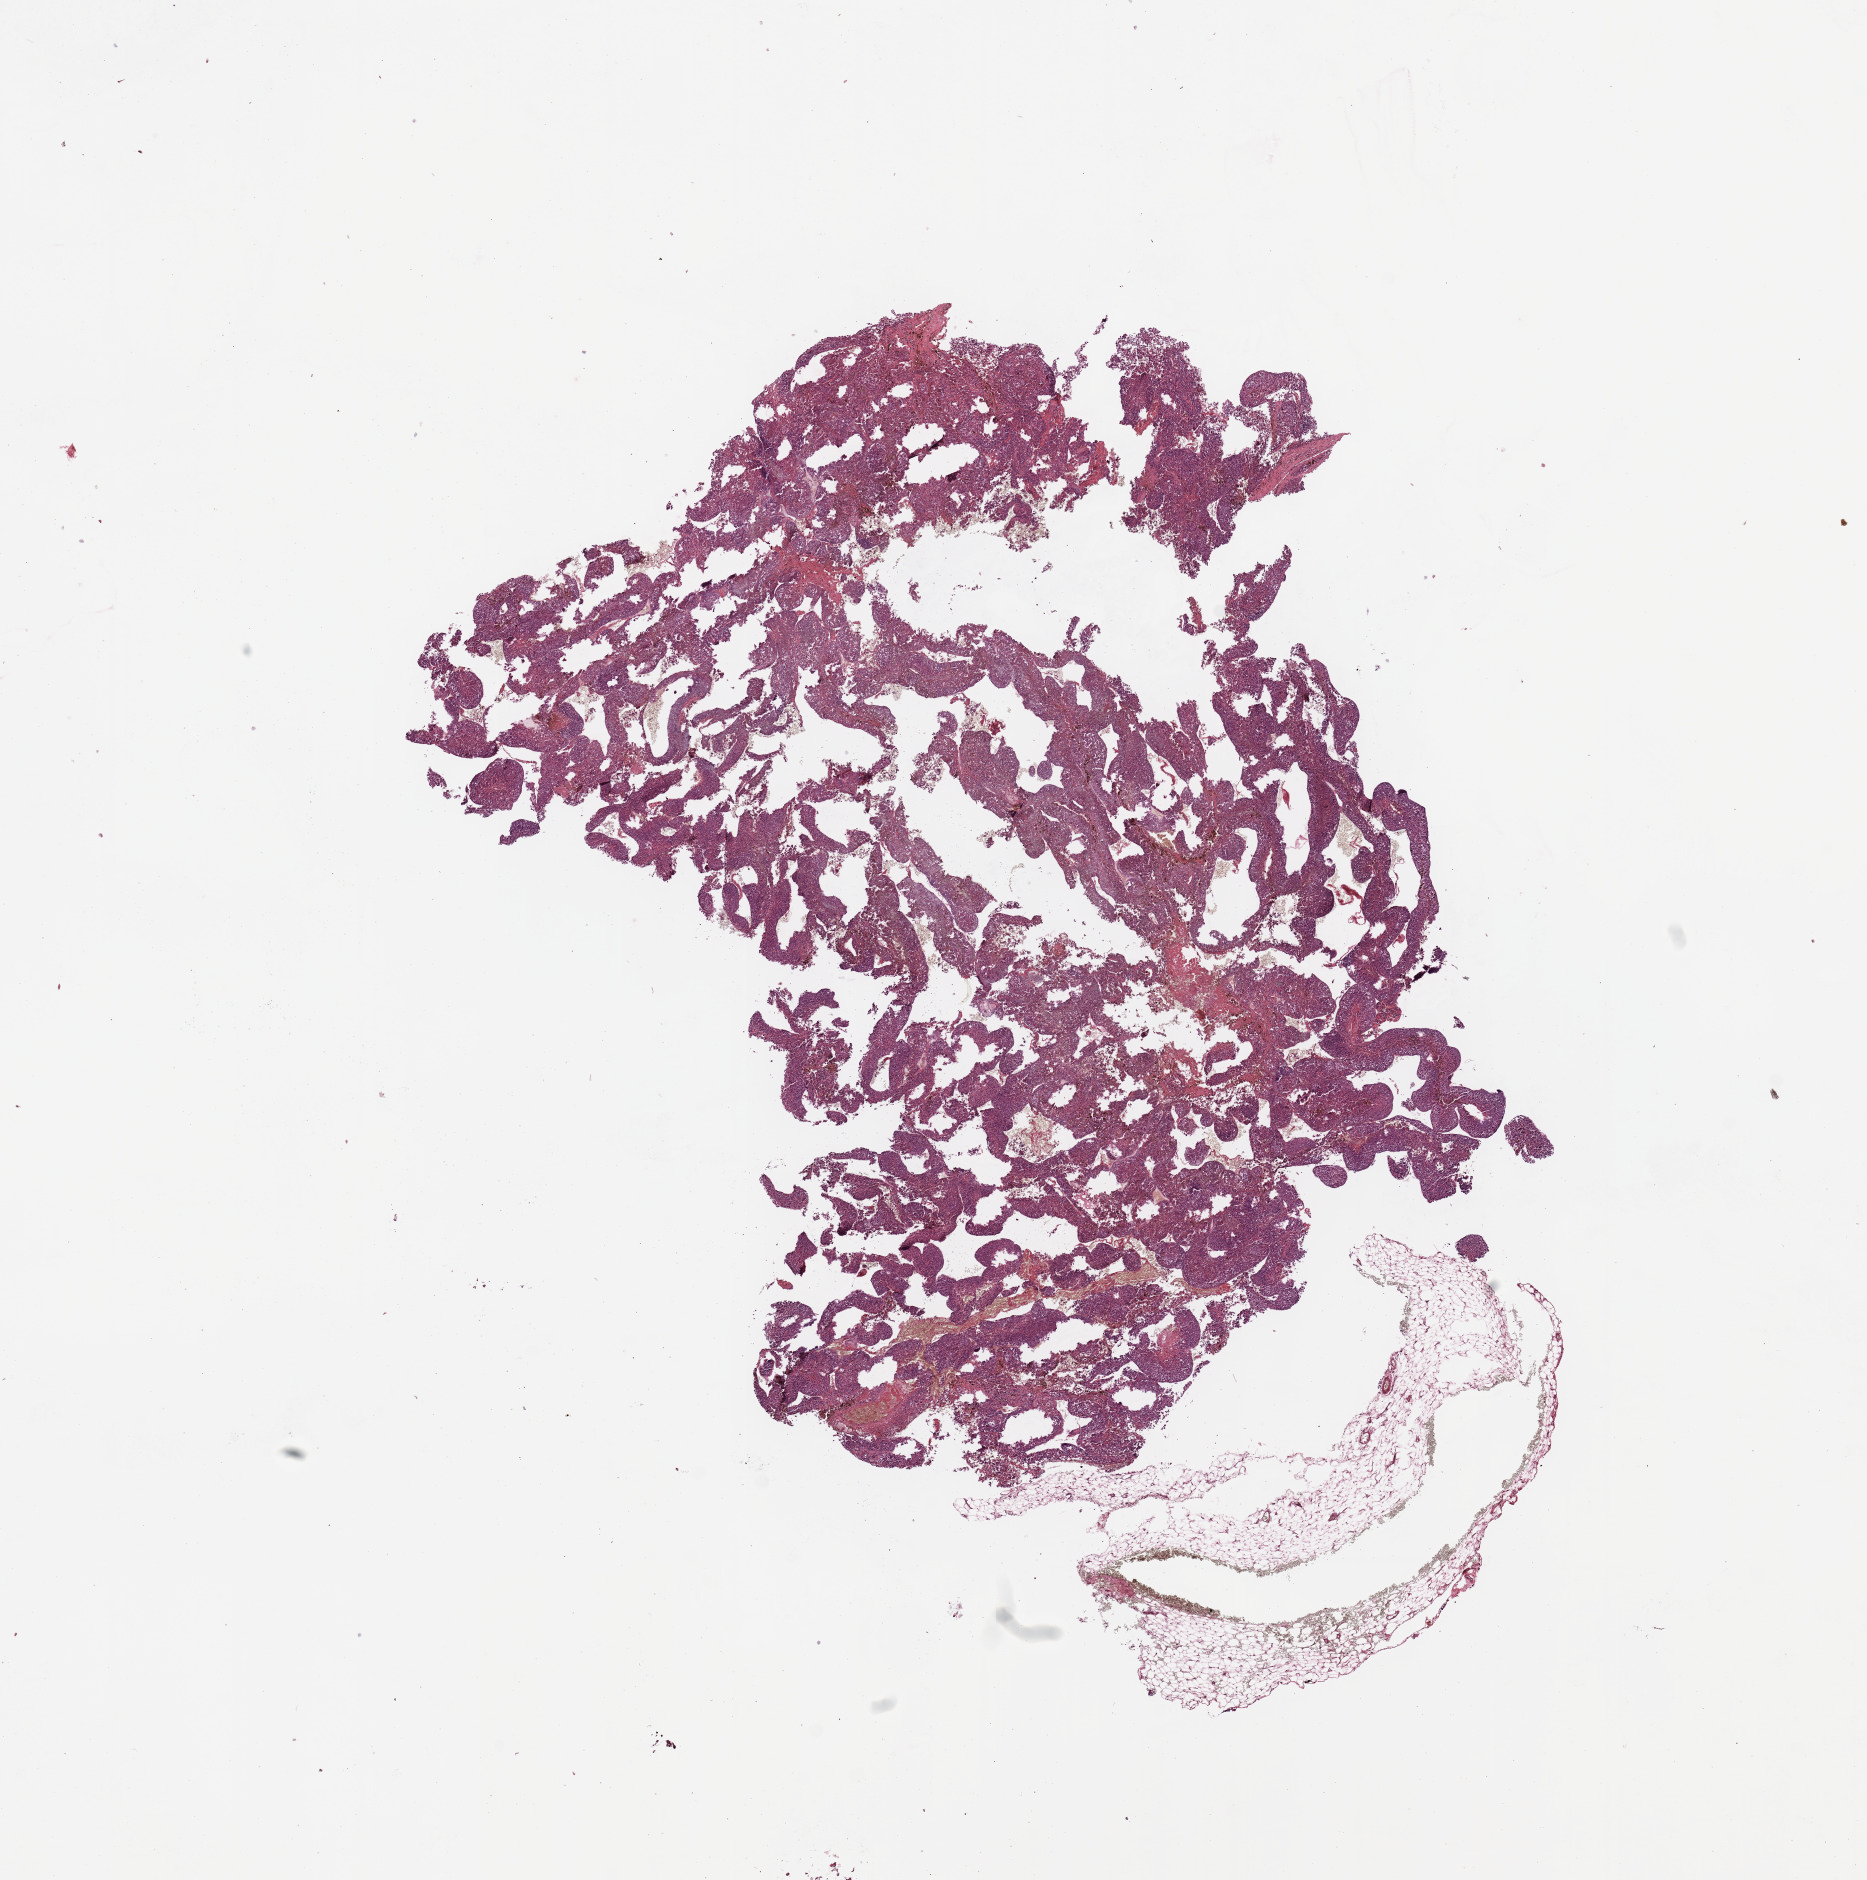
Digitized H&E tissue section (whole slide), a low-resolution overview of the entire scanned area, about 14.8 x 14.9 mm. Melanoma tumour tissue; sampled site not recorded. 60-year-old male patient.
Patient diagnosis (cohort enrolment): cutaneous melanoma (skin).